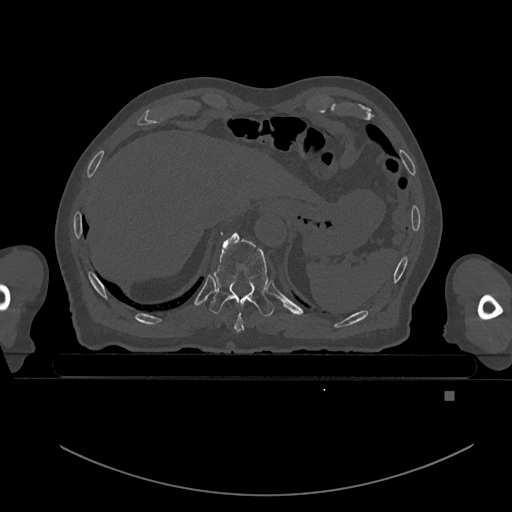
CT including the spine, one axial slice. Slice 100 of 969 in the series (ordered by position). Bone window (W 1800 / L 400 HU). 0.5 mm slice thickness. 512 × 512 image matrix, field of view 456 × 456 mm. Patient: male, 82 years. From the clinical record (not read from this slice): primary cancer: prostate.
Structures marked on this image (semi-automatic segmentation, software-assisted and operator-edited):
- T10 vertebra: bounding box <209,232,274,317> (left, top, right, bottom; pixels)
- T9 vertebra: <234,312,244,333>